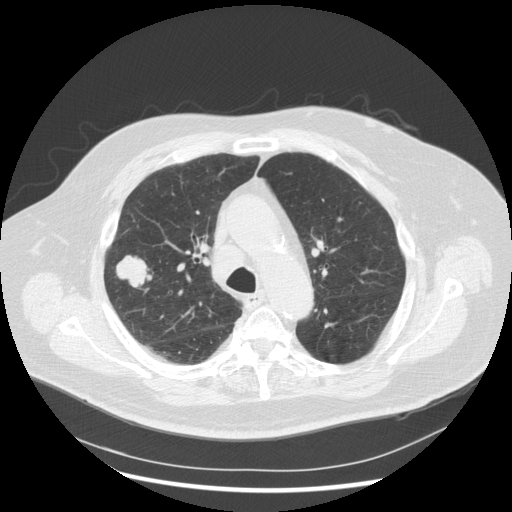
Low-dose screening chest CT, one axial slice; slice 194 of 263 in the series (ordered by position); reconstruction kernel STANDARD; 120 kVp; lung window (W 1500 / L -600 HU); 2.5 mm slice thickness; 512 × 512 image matrix, field of view 400 × 400 mm.
Annotated regions visible in this slice (outlined manually by an expert reader):
- lesion 1 (tumor, upper lobe of right lung): bounding box <116,256,152,287> (left, top, right, bottom; pixels)